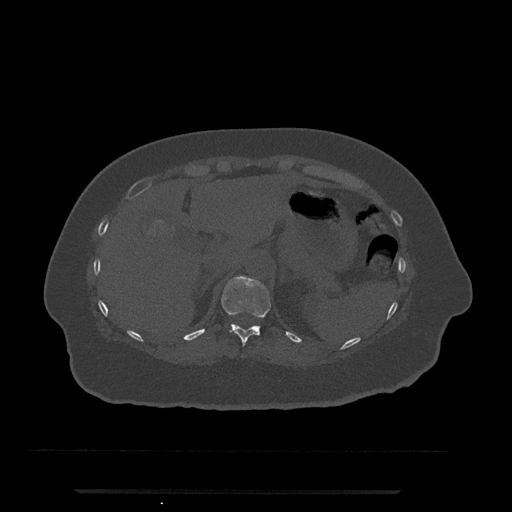
CT including the spine, one axial slice. Position 222 of 797 along the scan axis. 120 kVp. Bone window (W 1800 / L 400 HU). 0.5 mm slice thickness. 512 × 512 image matrix, field of view 440 × 440 mm. Patient: female, 51 years. From the clinical record (not read from this slice): primary cancer: neuro.
Structures marked on this image (semi-automatically segmented with operator editing):
- T11 vertebra: box from (x=221, y=276) to (x=271, y=346) px